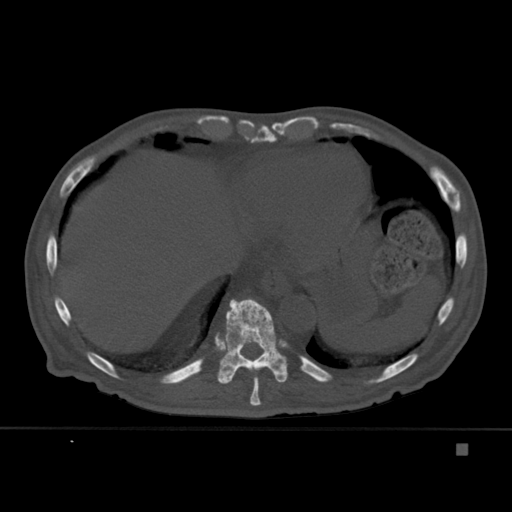
CT including the spine, one axial slice; slice 235 of 451 in the series (ordered by position); bone window (W 1800 / L 400 HU); 1.5 mm slice thickness; 512 × 512 image matrix. Patient: male, 75 years. From the clinical record (not read from this slice): primary cancer: prostate.
Outlined on this slice (semi-automatically segmented with operator editing):
- T10 vertebra: bounding box (x1, y1, x2, y2) in pixels: (216, 299, 288, 384)
- T9 vertebra: (236, 370, 262, 406)